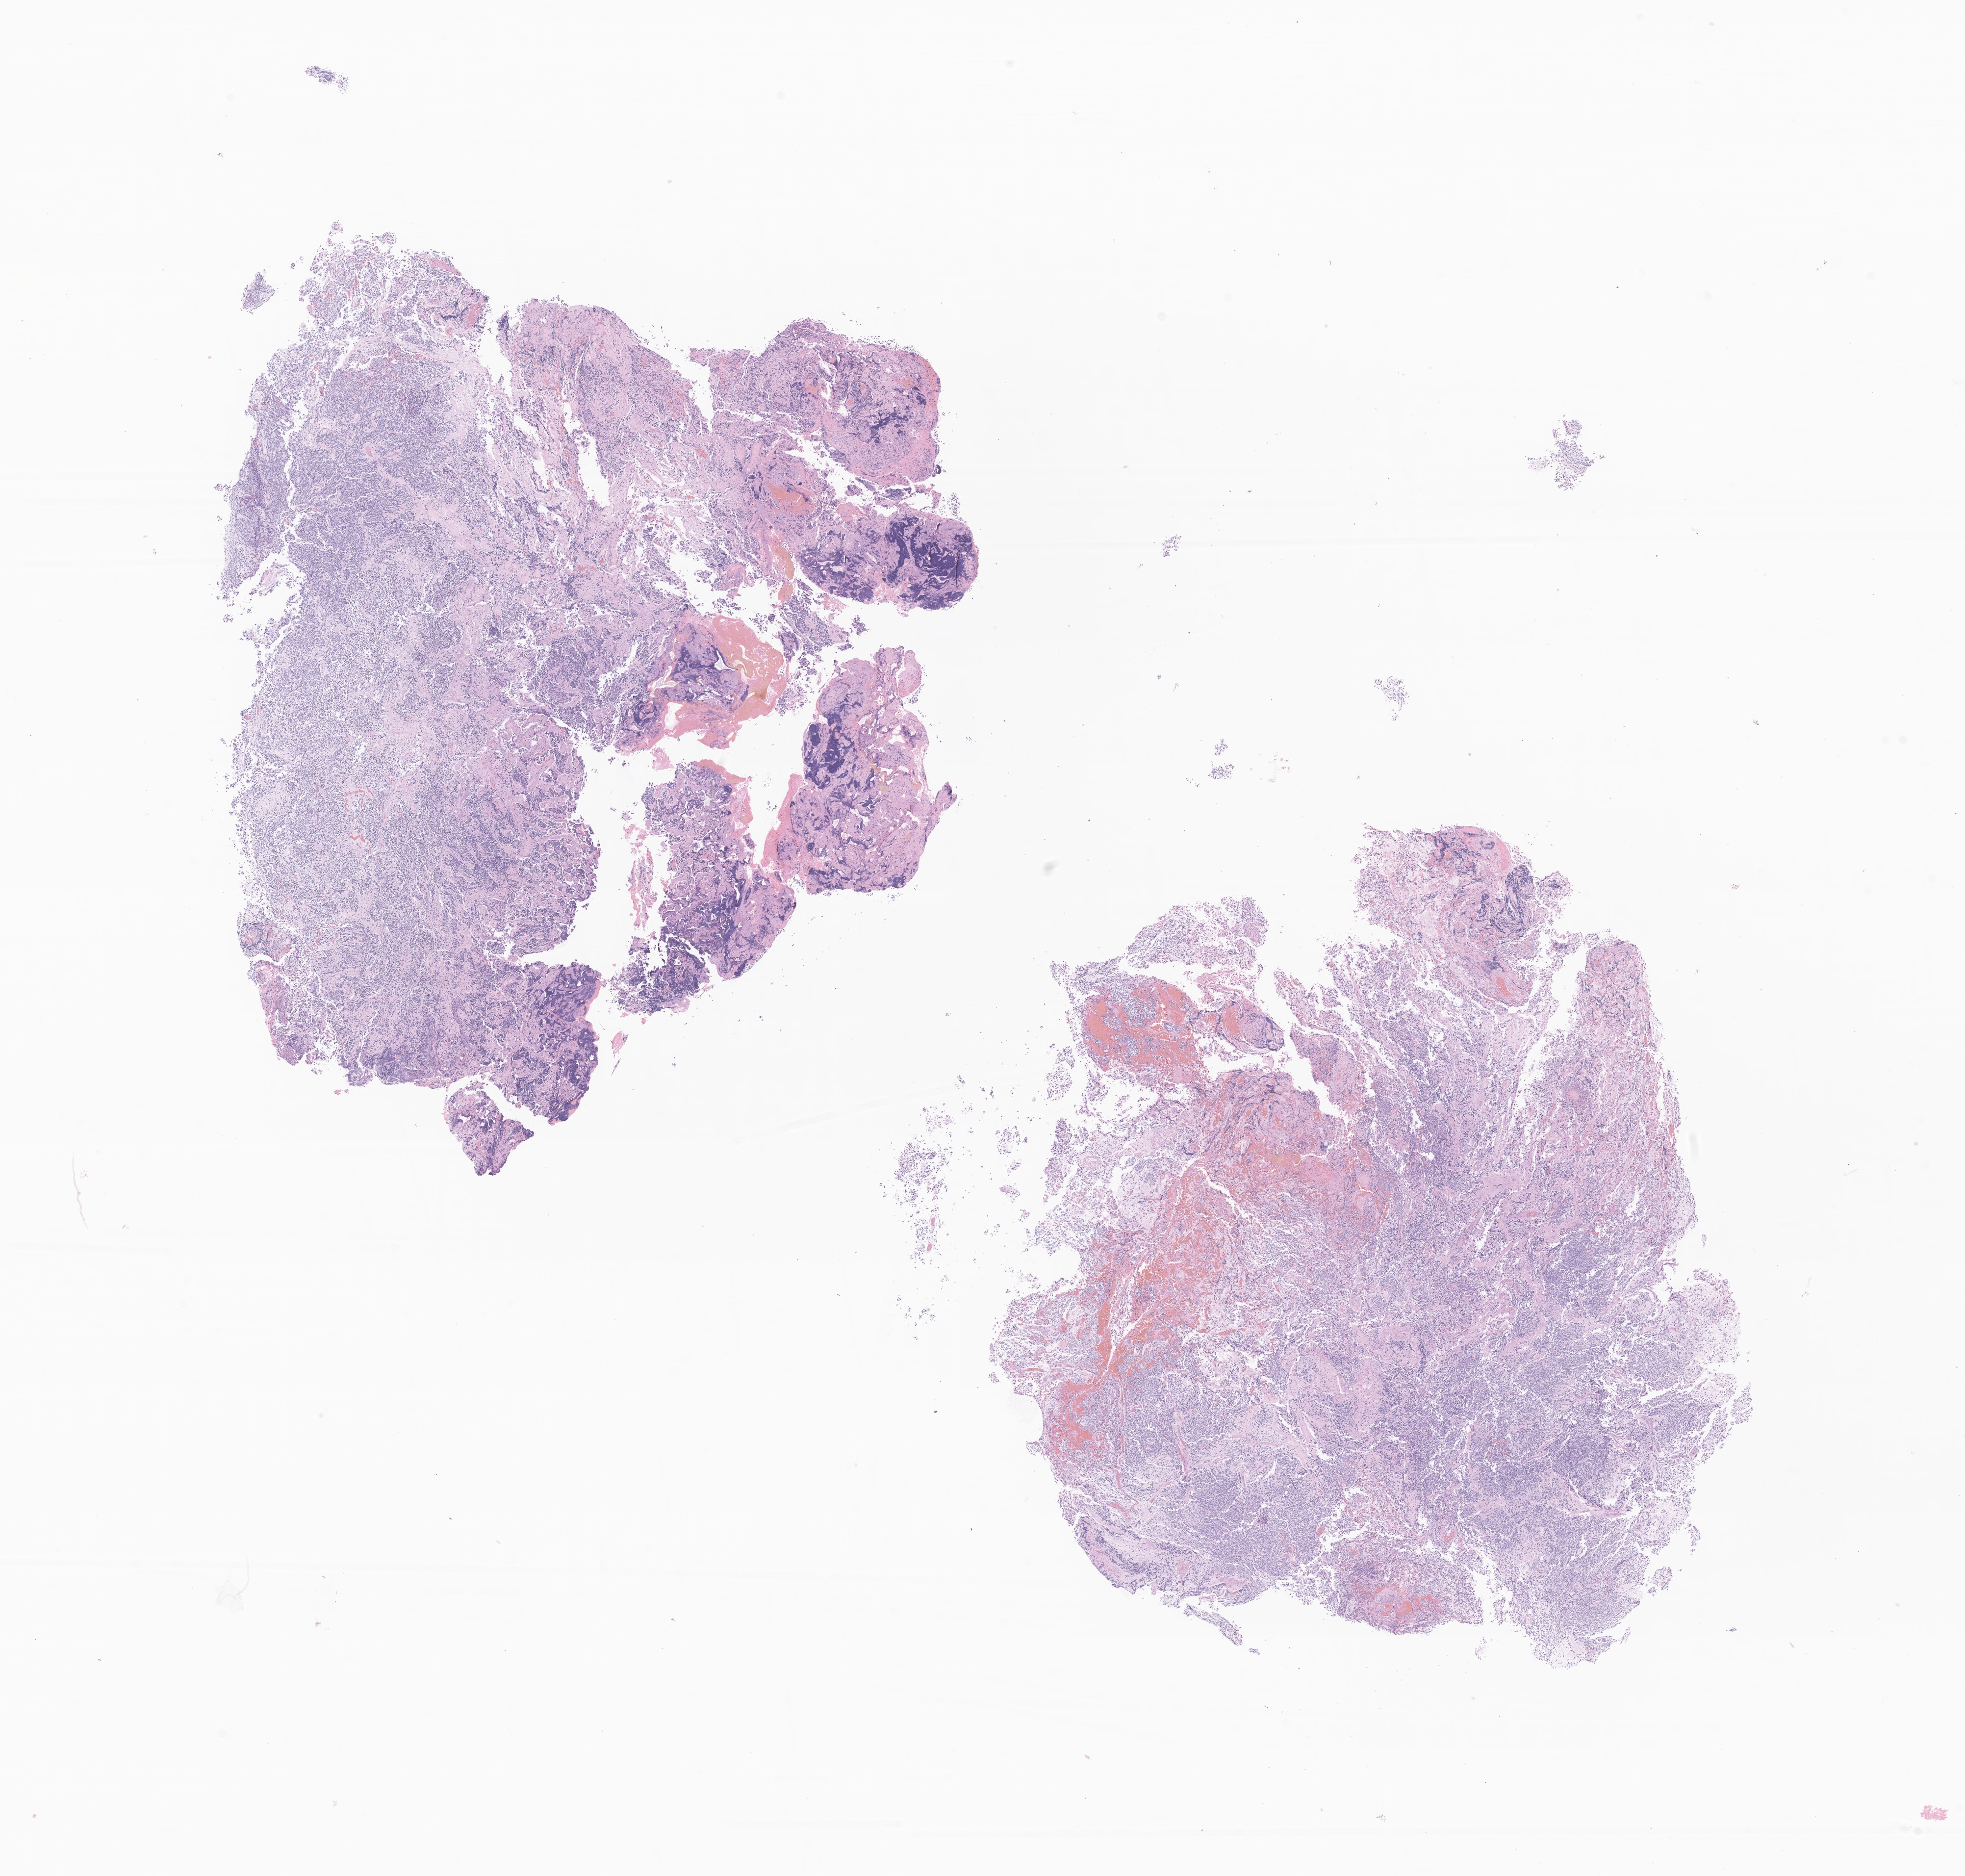
Digitized hematoxylin and eosin (H&E)-stained section of tumor tissue from the cerebellum — low-resolution overview of the scanned area, about 16.9 x 16.1 mm. Formalin-fixed paraffin-embedded section. Patient male; age 171 months (14 years 3 months).
Recorded diagnosis: Medulloblastoma, NOS.